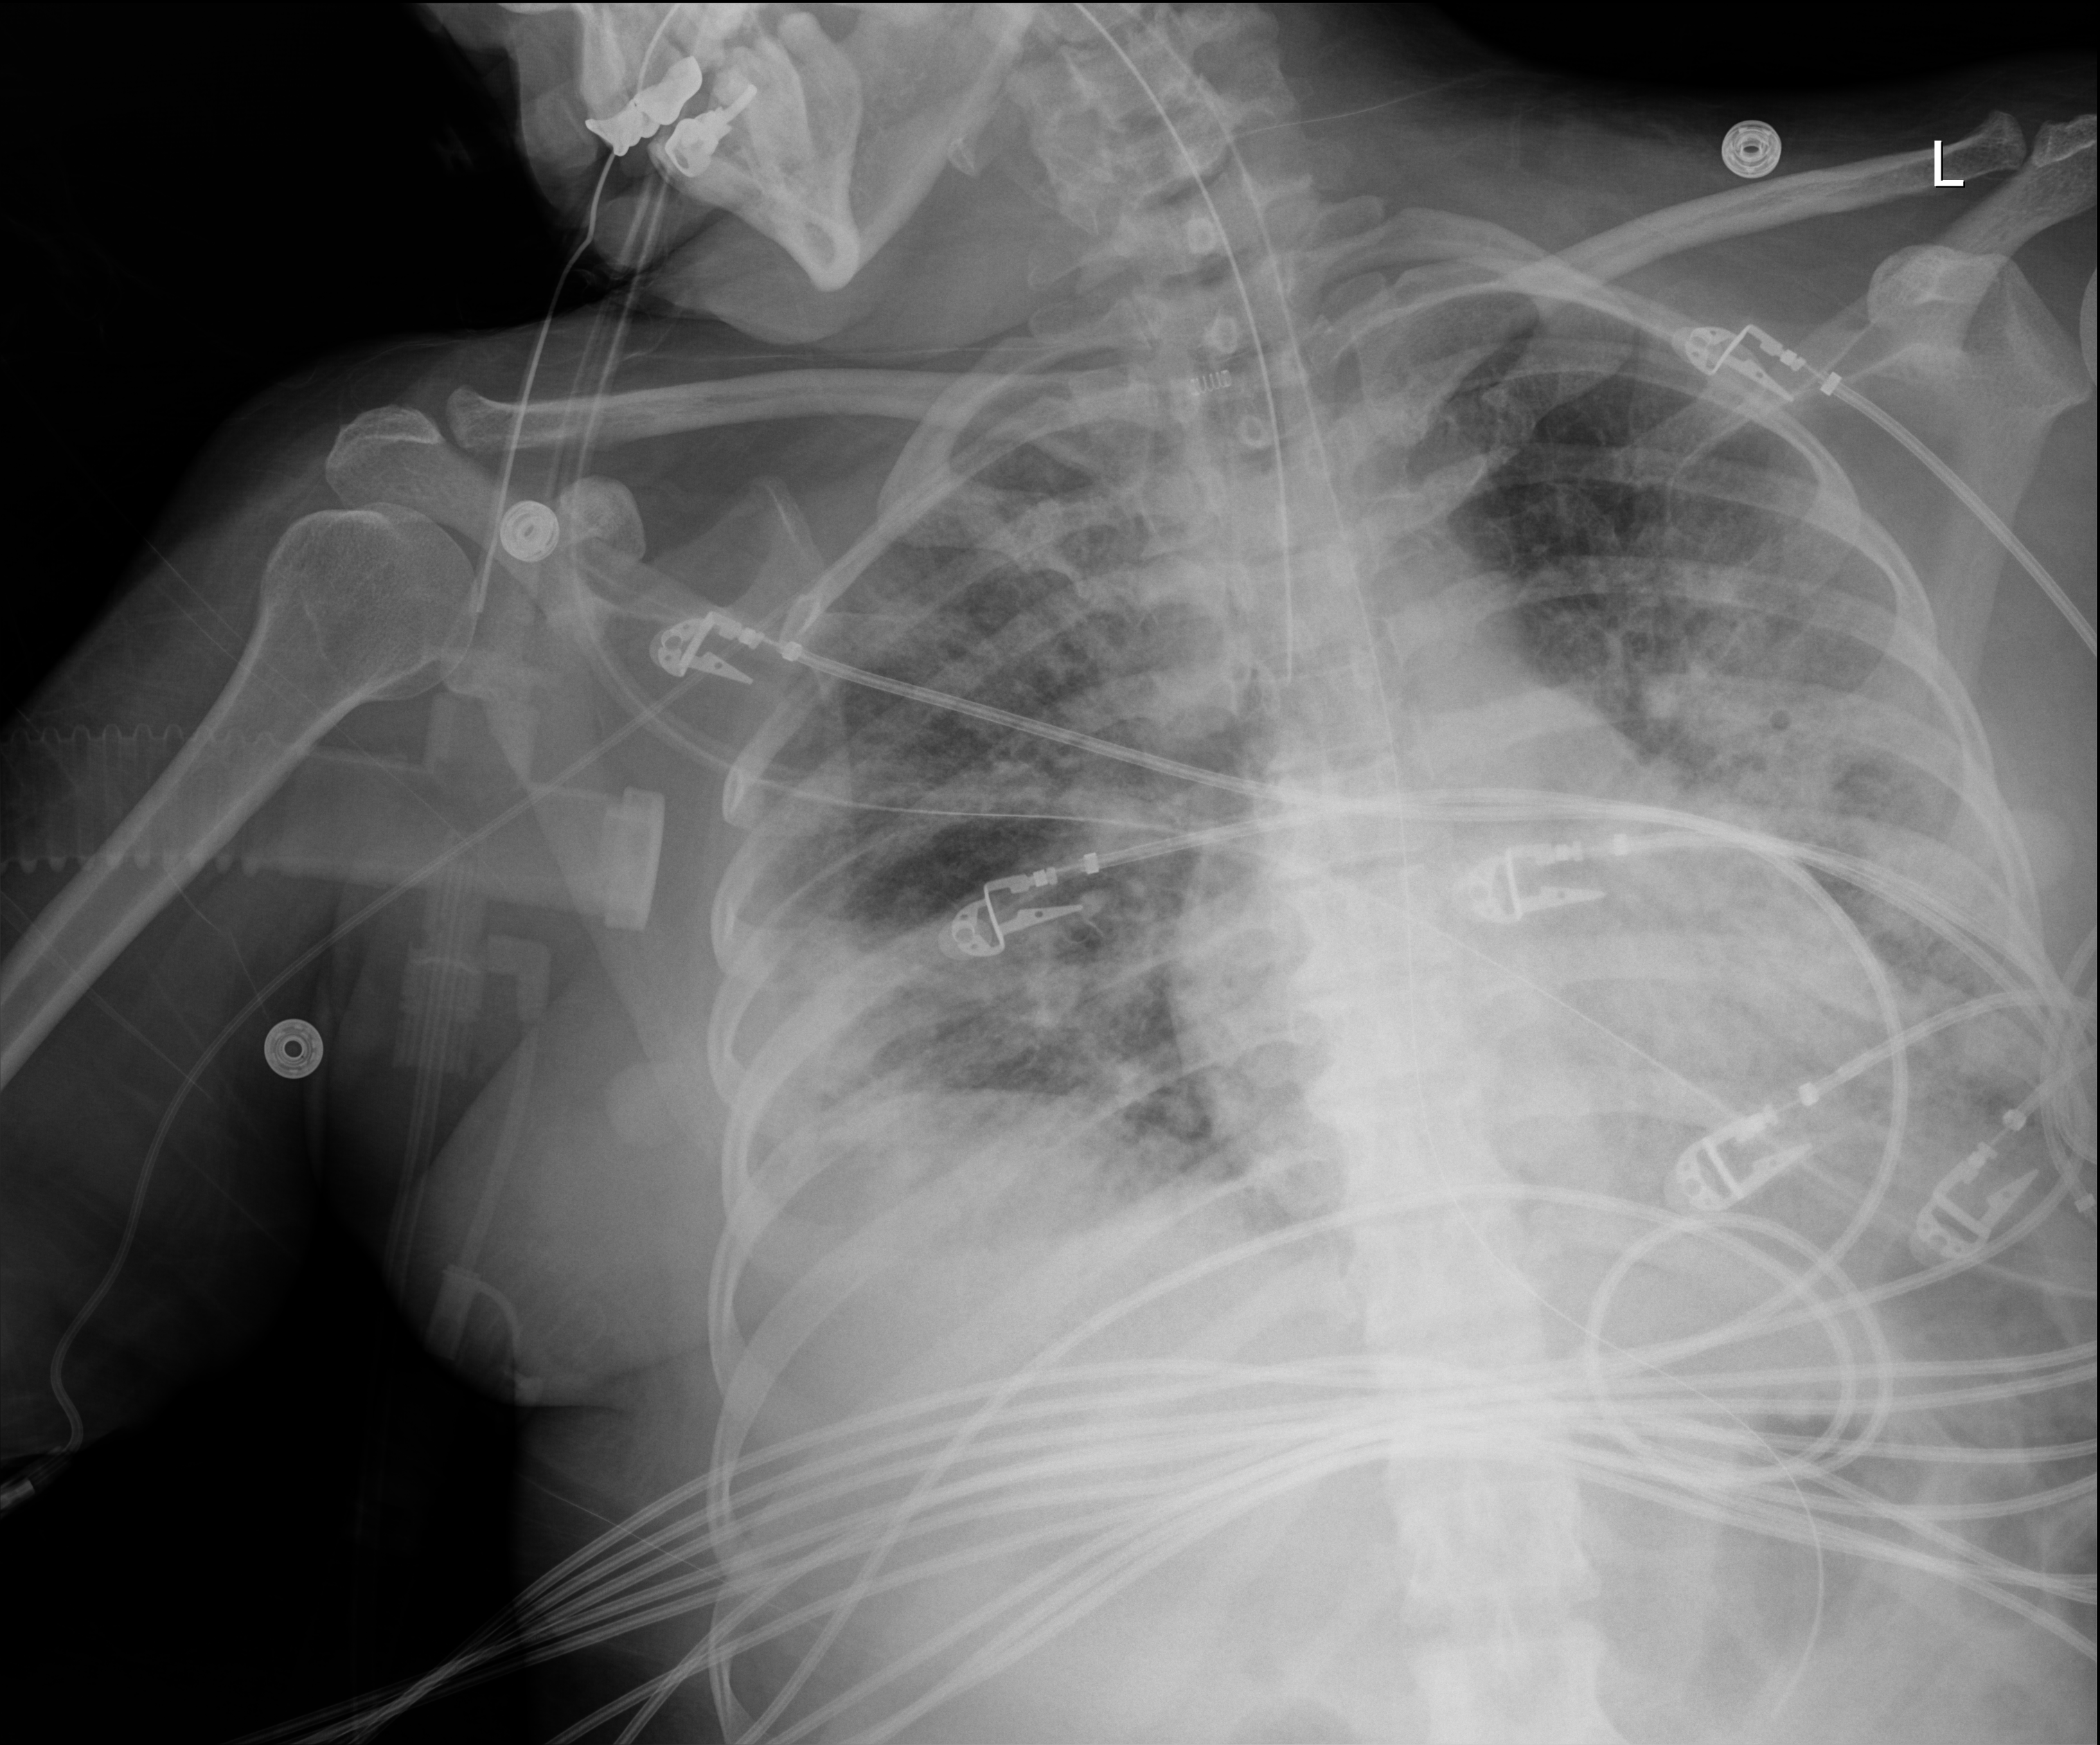
Portable chest radiograph, anteroposterior (AP) projection. Female patient hospitalised with COVID-19, age 18–59 years.
From the hospital-stay record, not from the radiograph (when in the stay this image was taken is not recorded):
- other chronic lung disease (admission record): no